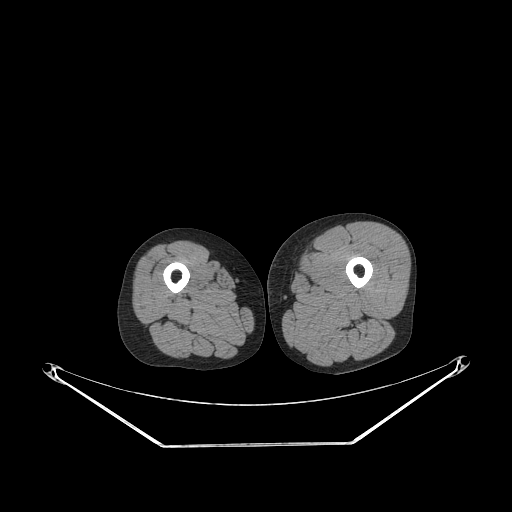
CT of an extremity soft-tissue mass (from a PET/CT study), one axial slice. Slice 236 of 267 in the series (ordered by position). Soft-tissue window (W 400 / L 40 HU). 3.75 mm slice thickness. 512 × 512 image matrix, field of view 500 × 500 mm. Male patient. Case-level facts recorded for this patient, not image findings: histological type: pleiomorphic leiomyosarcoma; grade: high; site of the primary tumour: left thigh.
Annotated regions visible in this slice (expert contour drawn on MRI and transferred to this co-registered scan by the dataset authors):
- gross tumour volume including surrounding oedema: bounding box (x1, y1, x2, y2) in pixels: (294, 265, 307, 280)